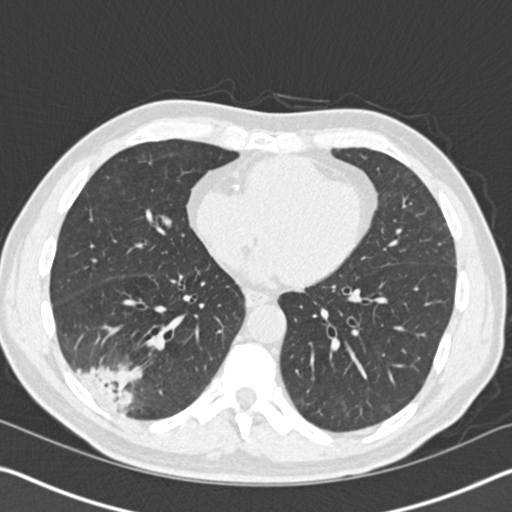
Axial slice from a low-dose chest CT screening exam. Baseline annual screen. Lung window (W 1500 / L -600 HU). Standard (soft-tissue) reconstruction kernel (B30f). 120 kVp. Slice 98 of 161 in the series. Male participant, aged 61 years at enrolment.
Expert reader's lesion annotation, bounding box [x1, y1, x2, y2] px = [44, 321, 156, 423]. Screening reader's record for this exam (one nodule recorded; not confirmed to be the boxed lesion): non-calcified nodule or mass ≥4 mm, right lower lobe, 52 × 36 mm, spiculated (stellate) margins, soft tissue attenuation. Official screen result: positive, change unspecified: nodule(s) >= 4 mm or enlarging nodule(s), mass(es), or other non-specific abnormalities suspicious for lung cancer. Later outcome: lung cancer diagnosed 392 days after this screen (after the second annual screen) — bronchiolo-alveolar adenocarcinoma, NOS, right lower lobe, moderately differentiated (G2), stage IIIB (AJCC 6th edition), 90 mm at pathology.